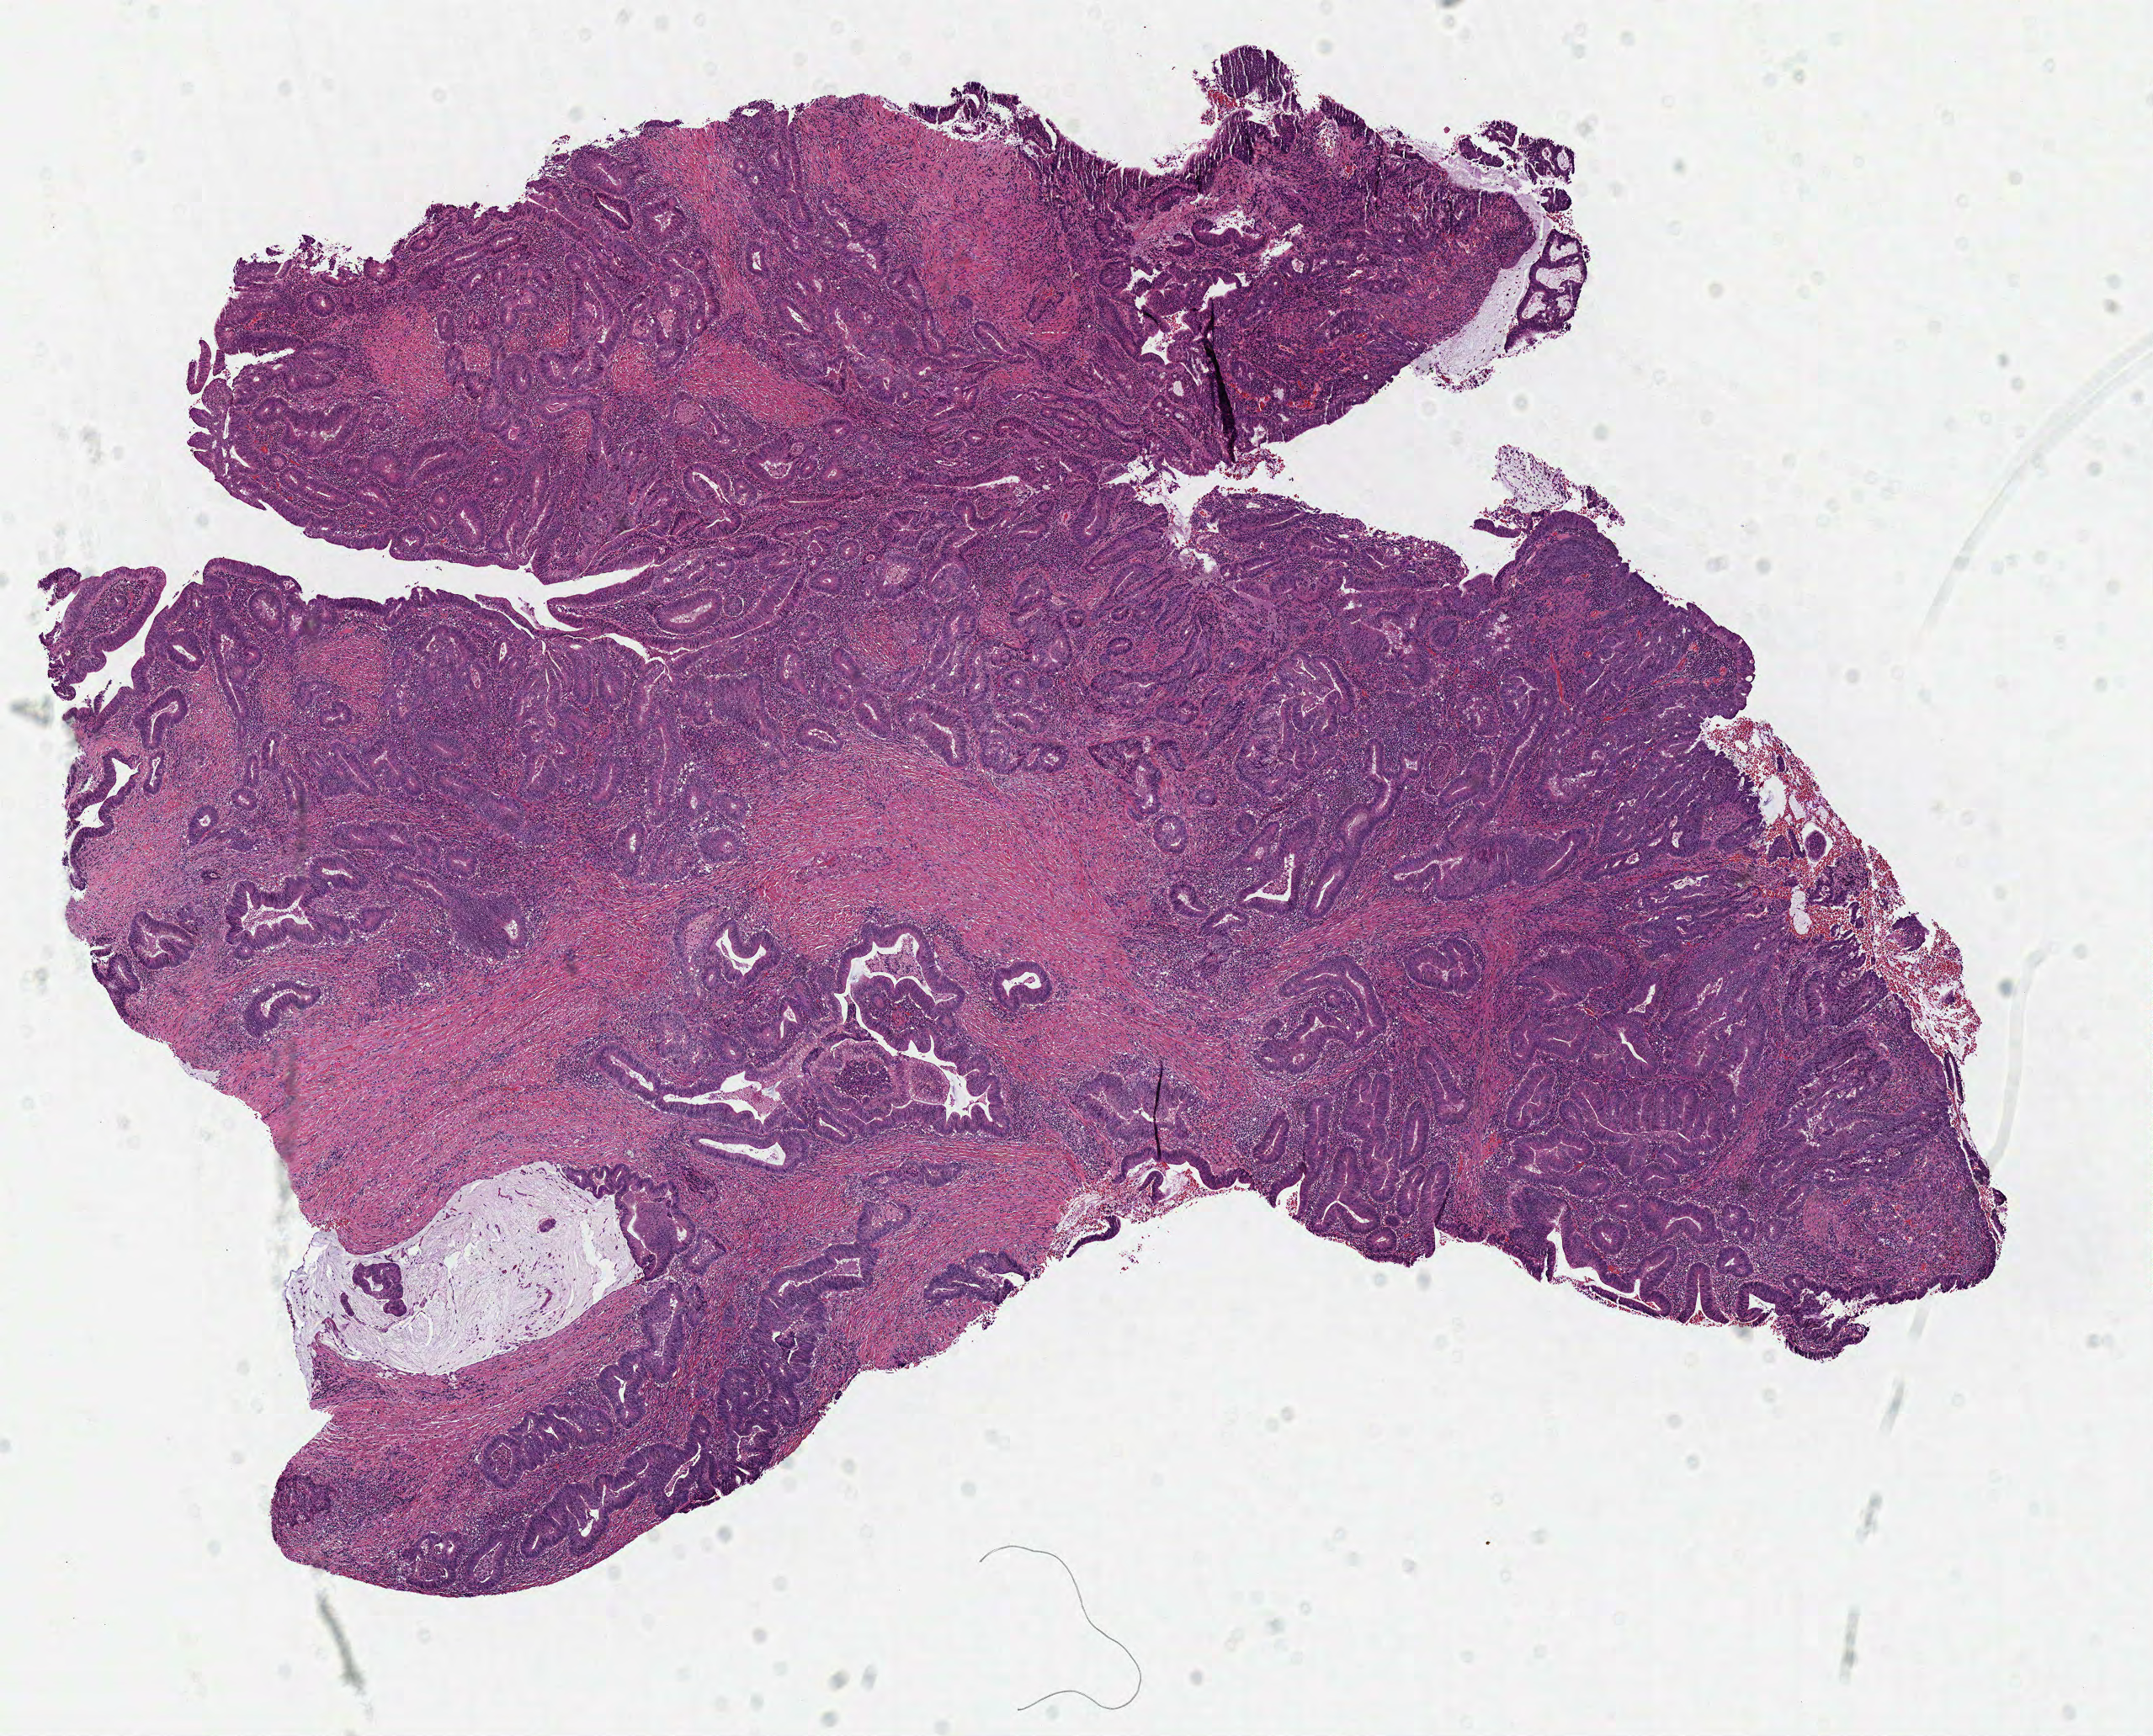
Whole-slide histology image, H&E — low-resolution overview of the scanned area, about 10.1 x 8.1 mm (from a 40x scan), frozen section from the top of the tissue portion, primary tumour sample from the colon. Male, age 31 years at initial diagnosis. Pathologist review of this section (percent, as recorded): tumour cells 99%, tumour nuclei 75%, normal cells 0%, stromal cells 0%, necrosis 1%. Infiltration values recorded for this section: lymphocyte infiltration 15%, monocyte infiltration 2%, neutrophil infiltration 5%.
AJCC pathologic stage: IIA. Lymph nodes positive (case pathology): 0 of 19 examined. Pathologic diagnosis: Adenocarcinoma, NOS.